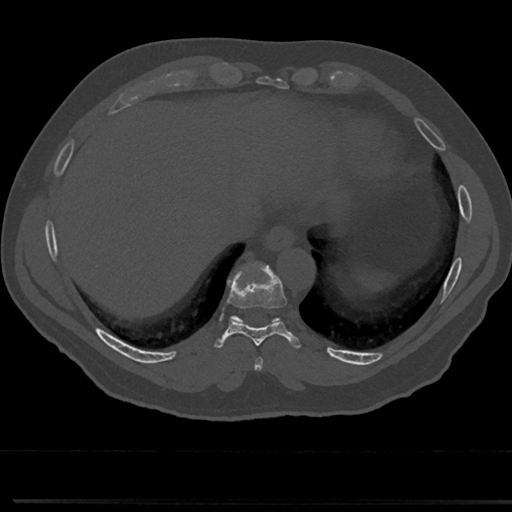
CT including the spine, one axial slice. Slice 297 of 817 in the series (ordered by position). Reconstruction kernel Br40s/3. 120 kVp. Bone window (W 1800 / L 400 HU). 0.5 mm slice thickness. 512 × 512 image matrix, field of view 355 × 355 mm. Male patient, age 61 years. Case-level facts recorded for this patient, not image findings: primary cancer: prostate.
Outlined on this slice (semi-automatically segmented with operator editing):
- T8 vertebra: box from (x=244, y=328) to (x=279, y=358) px
- T9 vertebra: (x=231, y=266)–(x=284, y=331)